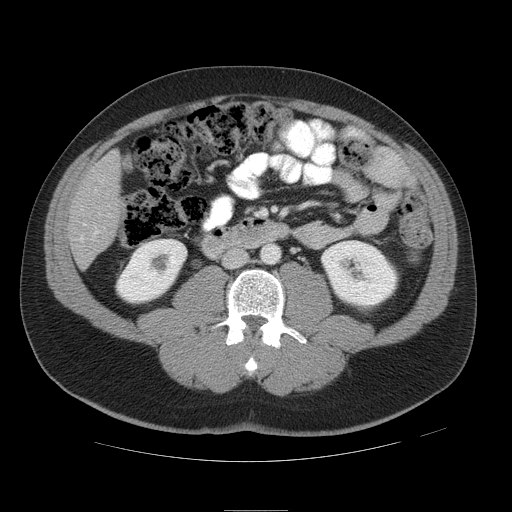
Contrast-enhanced abdominal CT, one axial slice; slice 14 of 49 in the series (ordered by position); reconstruction kernel STANDARD; intravenous contrast given; soft-tissue window (W 400 / L 40 HU); 5 mm slice thickness; 512 × 512 image matrix. Male patient, age 52 years. From the clinical record (not read from this slice): diagnosis: colorectal cancer liver metastases, imaged before liver resection; multiple liver metastases: yes; largest metastasis: 5.1 cm.
Structures marked on this image (expert manual segmentation):
- hepatic veins: bounding box (x1, y1, x2, y2) in pixels: (81, 224, 85, 240)
- liver: (69, 156, 119, 265)
- portal vein (with intrahepatic branches): (94, 189, 99, 234)